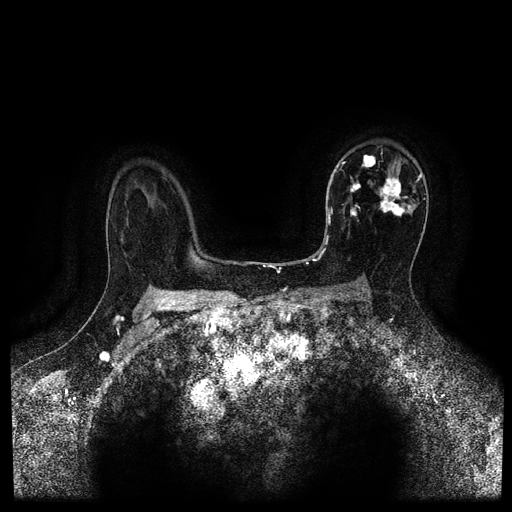
Breast MRI (dynamic contrast-enhanced, multi-phase), one axial slice. Slice 71 of 116 in the series (ordered by position). Dynamic contrast-enhanced series, time point 2 of 5 at this slice position (early post-contrast). 1.5 T. TE 2.7 ms, TR 5.4 ms. 512 × 512 image matrix, field of view 340 × 340 mm. Patient: female, 50 years.
Structures marked on this image (semi-automatic segmentation, software-assisted and operator-edited):
- breast lesion (labelled 'tumour' in the annotation; benign lesions carry a separate 'benign' label): bounding box <348,174,413,222> (left, top, right, bottom; pixels)
- breast lesion (labelled 'tumour' in the annotation; benign lesions carry a separate 'benign' label): <361,154,379,171>